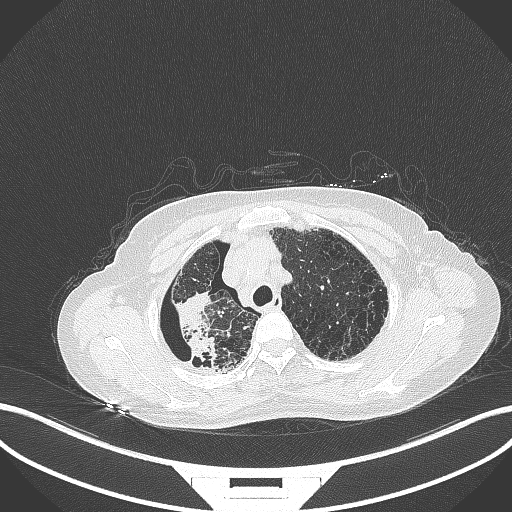
Chest CT, one axial slice. Position 290 of 408 along the scan axis. Reconstruction kernel B70f. Lung window (W 1500 / L -600 HU). 1 mm slice thickness. 512 × 512 image matrix, field of view 400 × 400 mm. Female patient, age 64 years. From the clinical record (not read from this slice): clinical TNM (as recorded): T3 N3 M0.
Outlined on this slice (rectangle marked by the reading radiologist):
- lung tumour (recorded histology: squamous cell carcinoma): bounding box (x1, y1, x2, y2) in pixels: (166, 283, 224, 371)